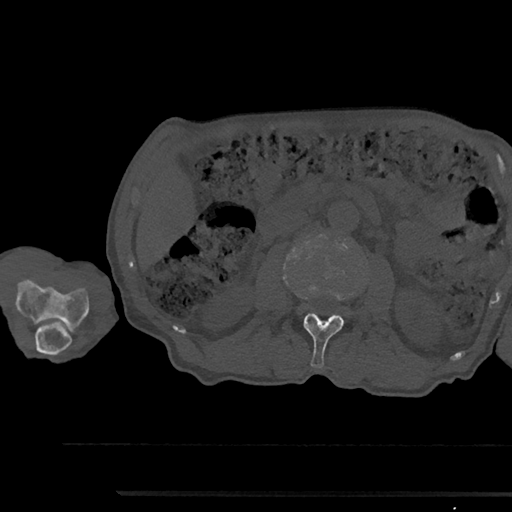
CT including the spine, one axial slice; position 539 of 797 along the scan axis; reconstruction kernel Br40s/3; bone window (W 1800 / L 400 HU); 0.5 mm slice thickness; 512 × 512 image matrix, field of view 367 × 367 mm. Patient: male, 79 years. Case-level facts recorded for this patient, not image findings: primary cancer: prostate.
Structures marked on this image (semi-automatically segmented with operator editing):
- L2 vertebra: bounding box (x1, y1, x2, y2) in pixels: (304, 293, 346, 368)